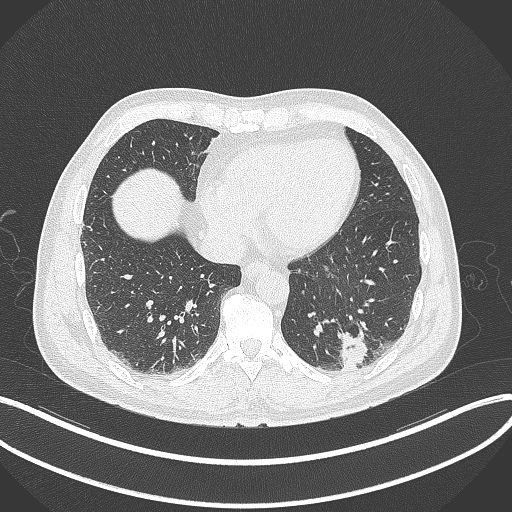
Chest CT, one axial slice; position 84 of 300 along the scan axis; 120 kVp; lung window (W 1500 / L -600 HU); 1 mm slice thickness; 512 × 512 image matrix, field of view 400 × 400 mm. Male patient, age 54 years. Case-level facts recorded for this patient, not image findings: clinical TNM (as recorded): T1c N0 M1.
Structures marked on this image (bounding box drawn by a radiologist):
- lung tumour (recorded histology: adenocarcinoma): box from (x=337, y=330) to (x=371, y=371) px